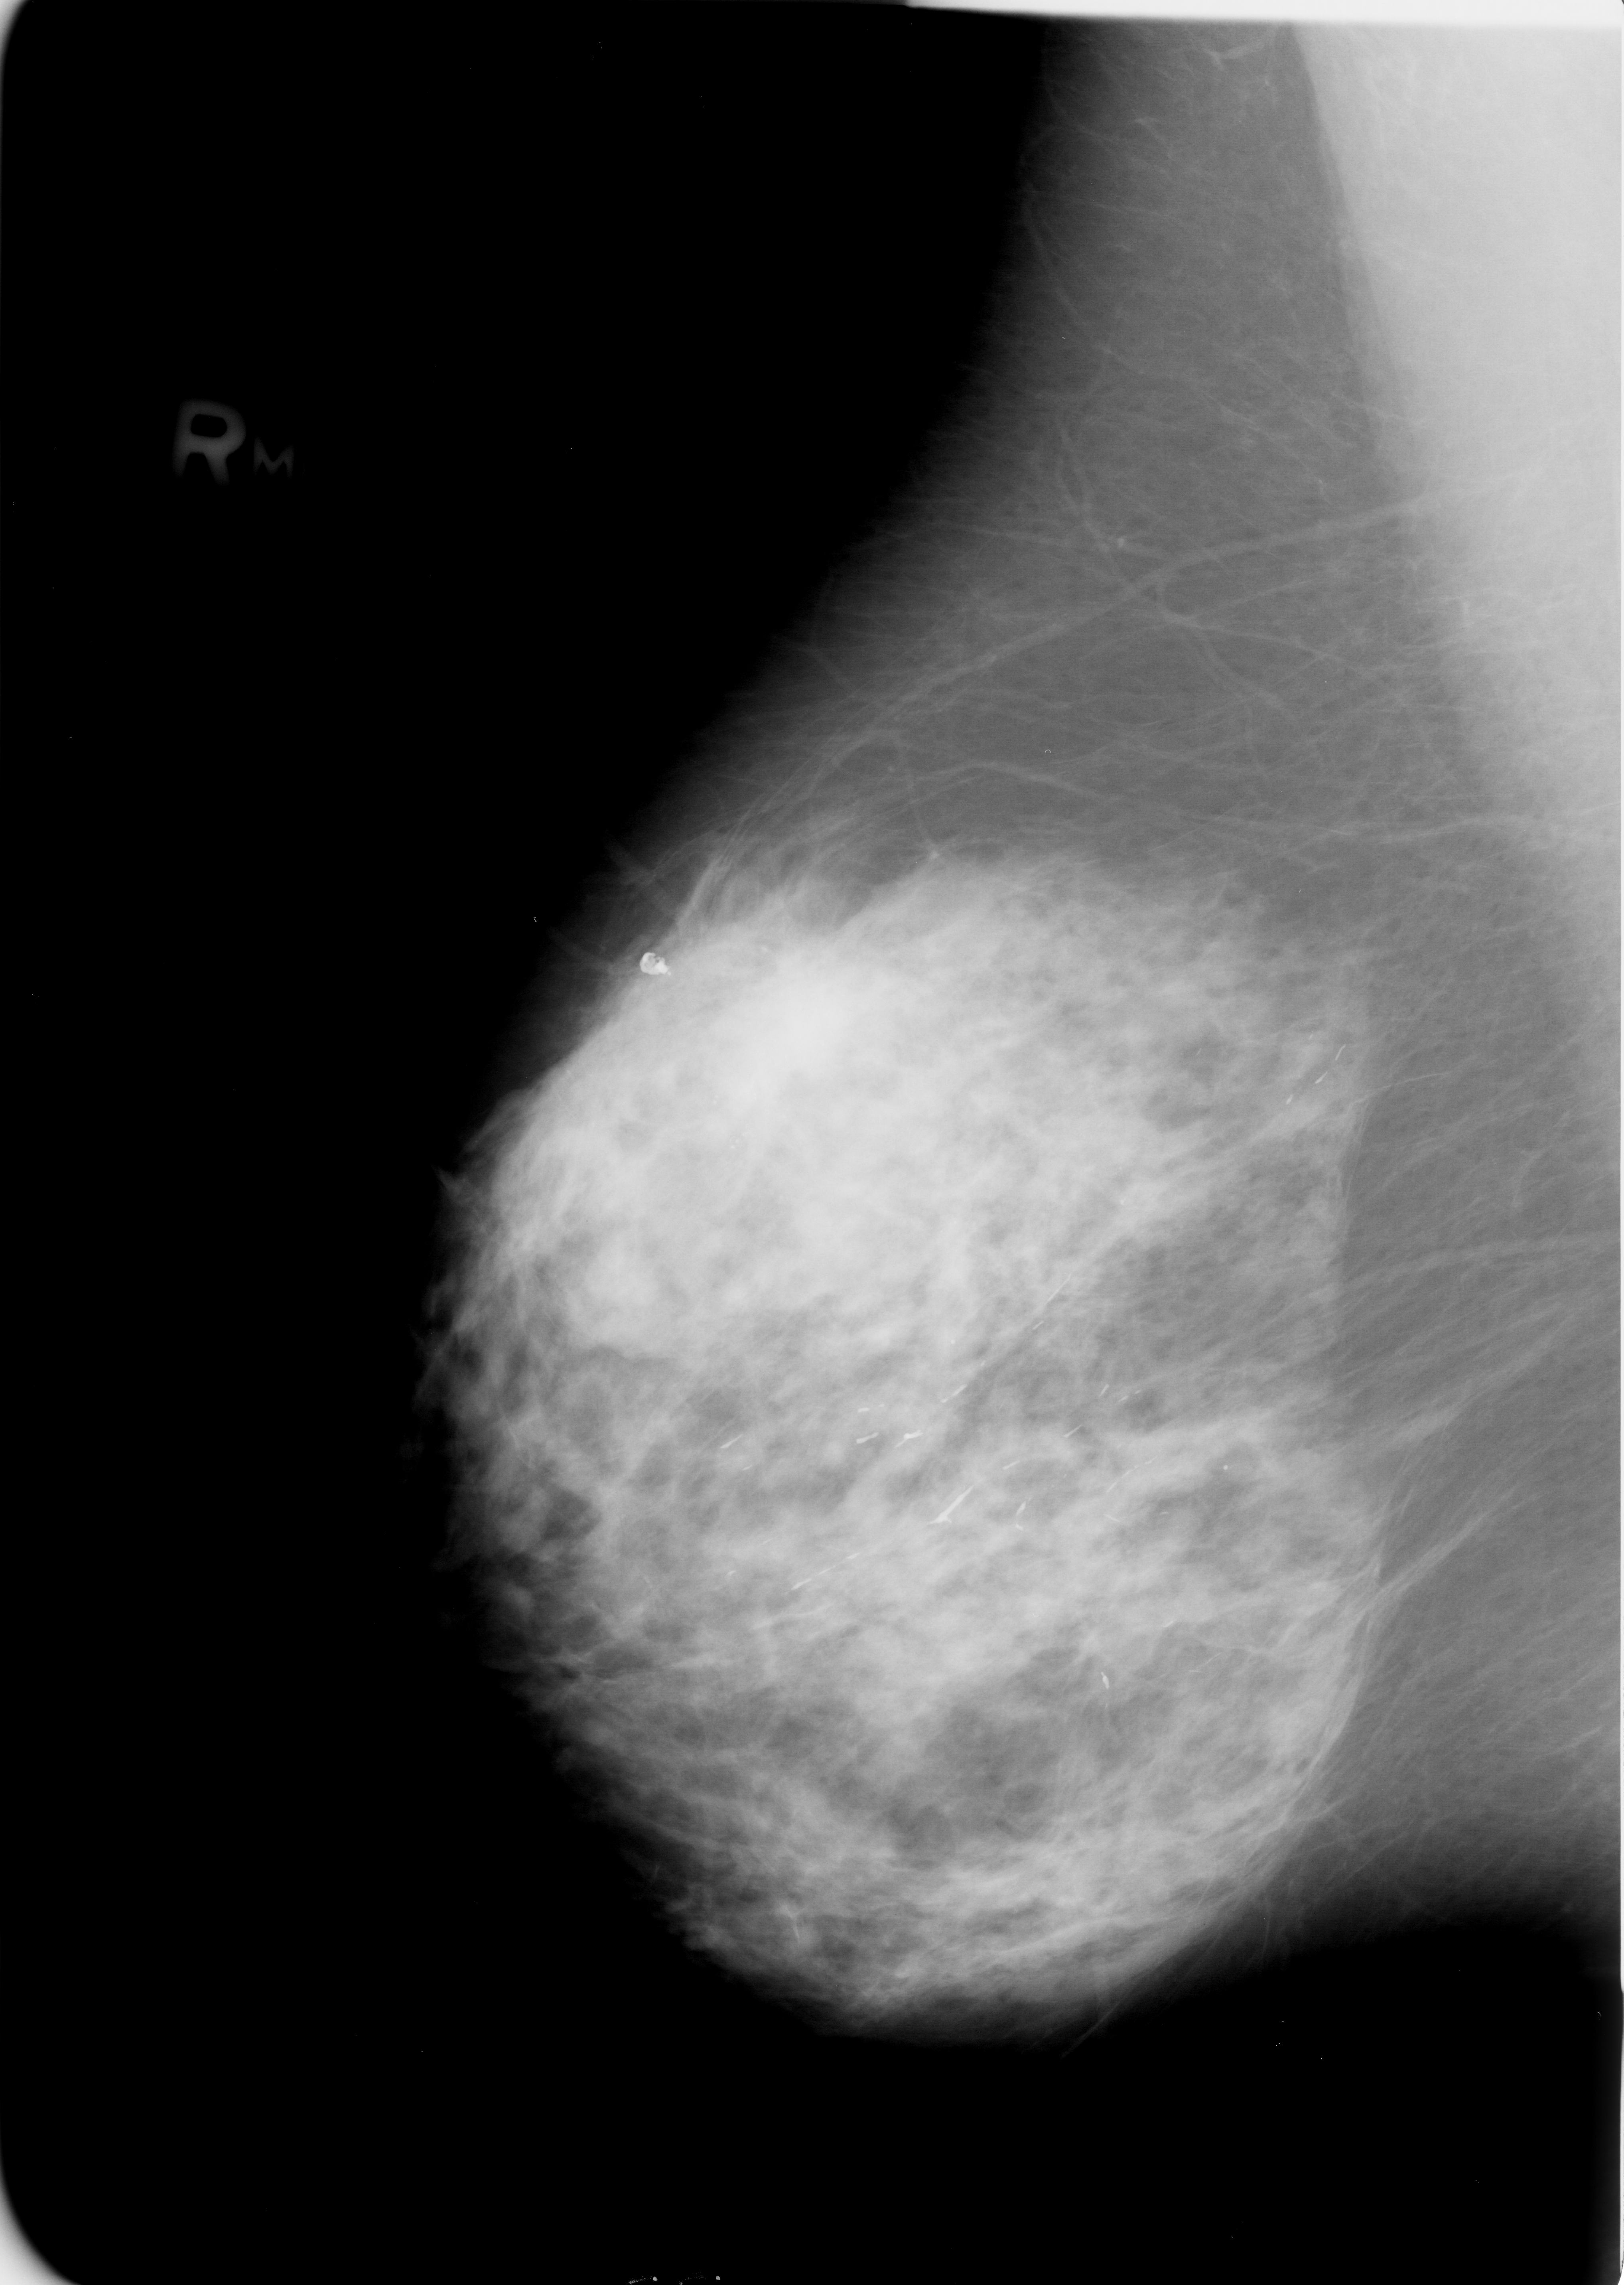
Digitized screen-film mammogram, right breast, MLO view, BI-RADS breast density category 3 (scale 1–4).
Marked findings (only marked abnormalities are described; nothing is implied about the rest of the image): Finding 1 of 3: calcifications, morphology pleomorphic, distribution clustered; BI-RADS assessment category 4; pathology result (as recorded, not read from the image): malignant. Finding 2 of 3: calcifications, morphology pleomorphic, distribution clustered; BI-RADS assessment category 4; pathology result (as recorded, not read from the image): malignant. Finding 3 of 3: calcifications, morphology pleomorphic, distribution clustered; BI-RADS assessment category 4; subtlety rating 3 on a 1 (subtle) to 5 (obvious) scale; pathology (as recorded): malignant.